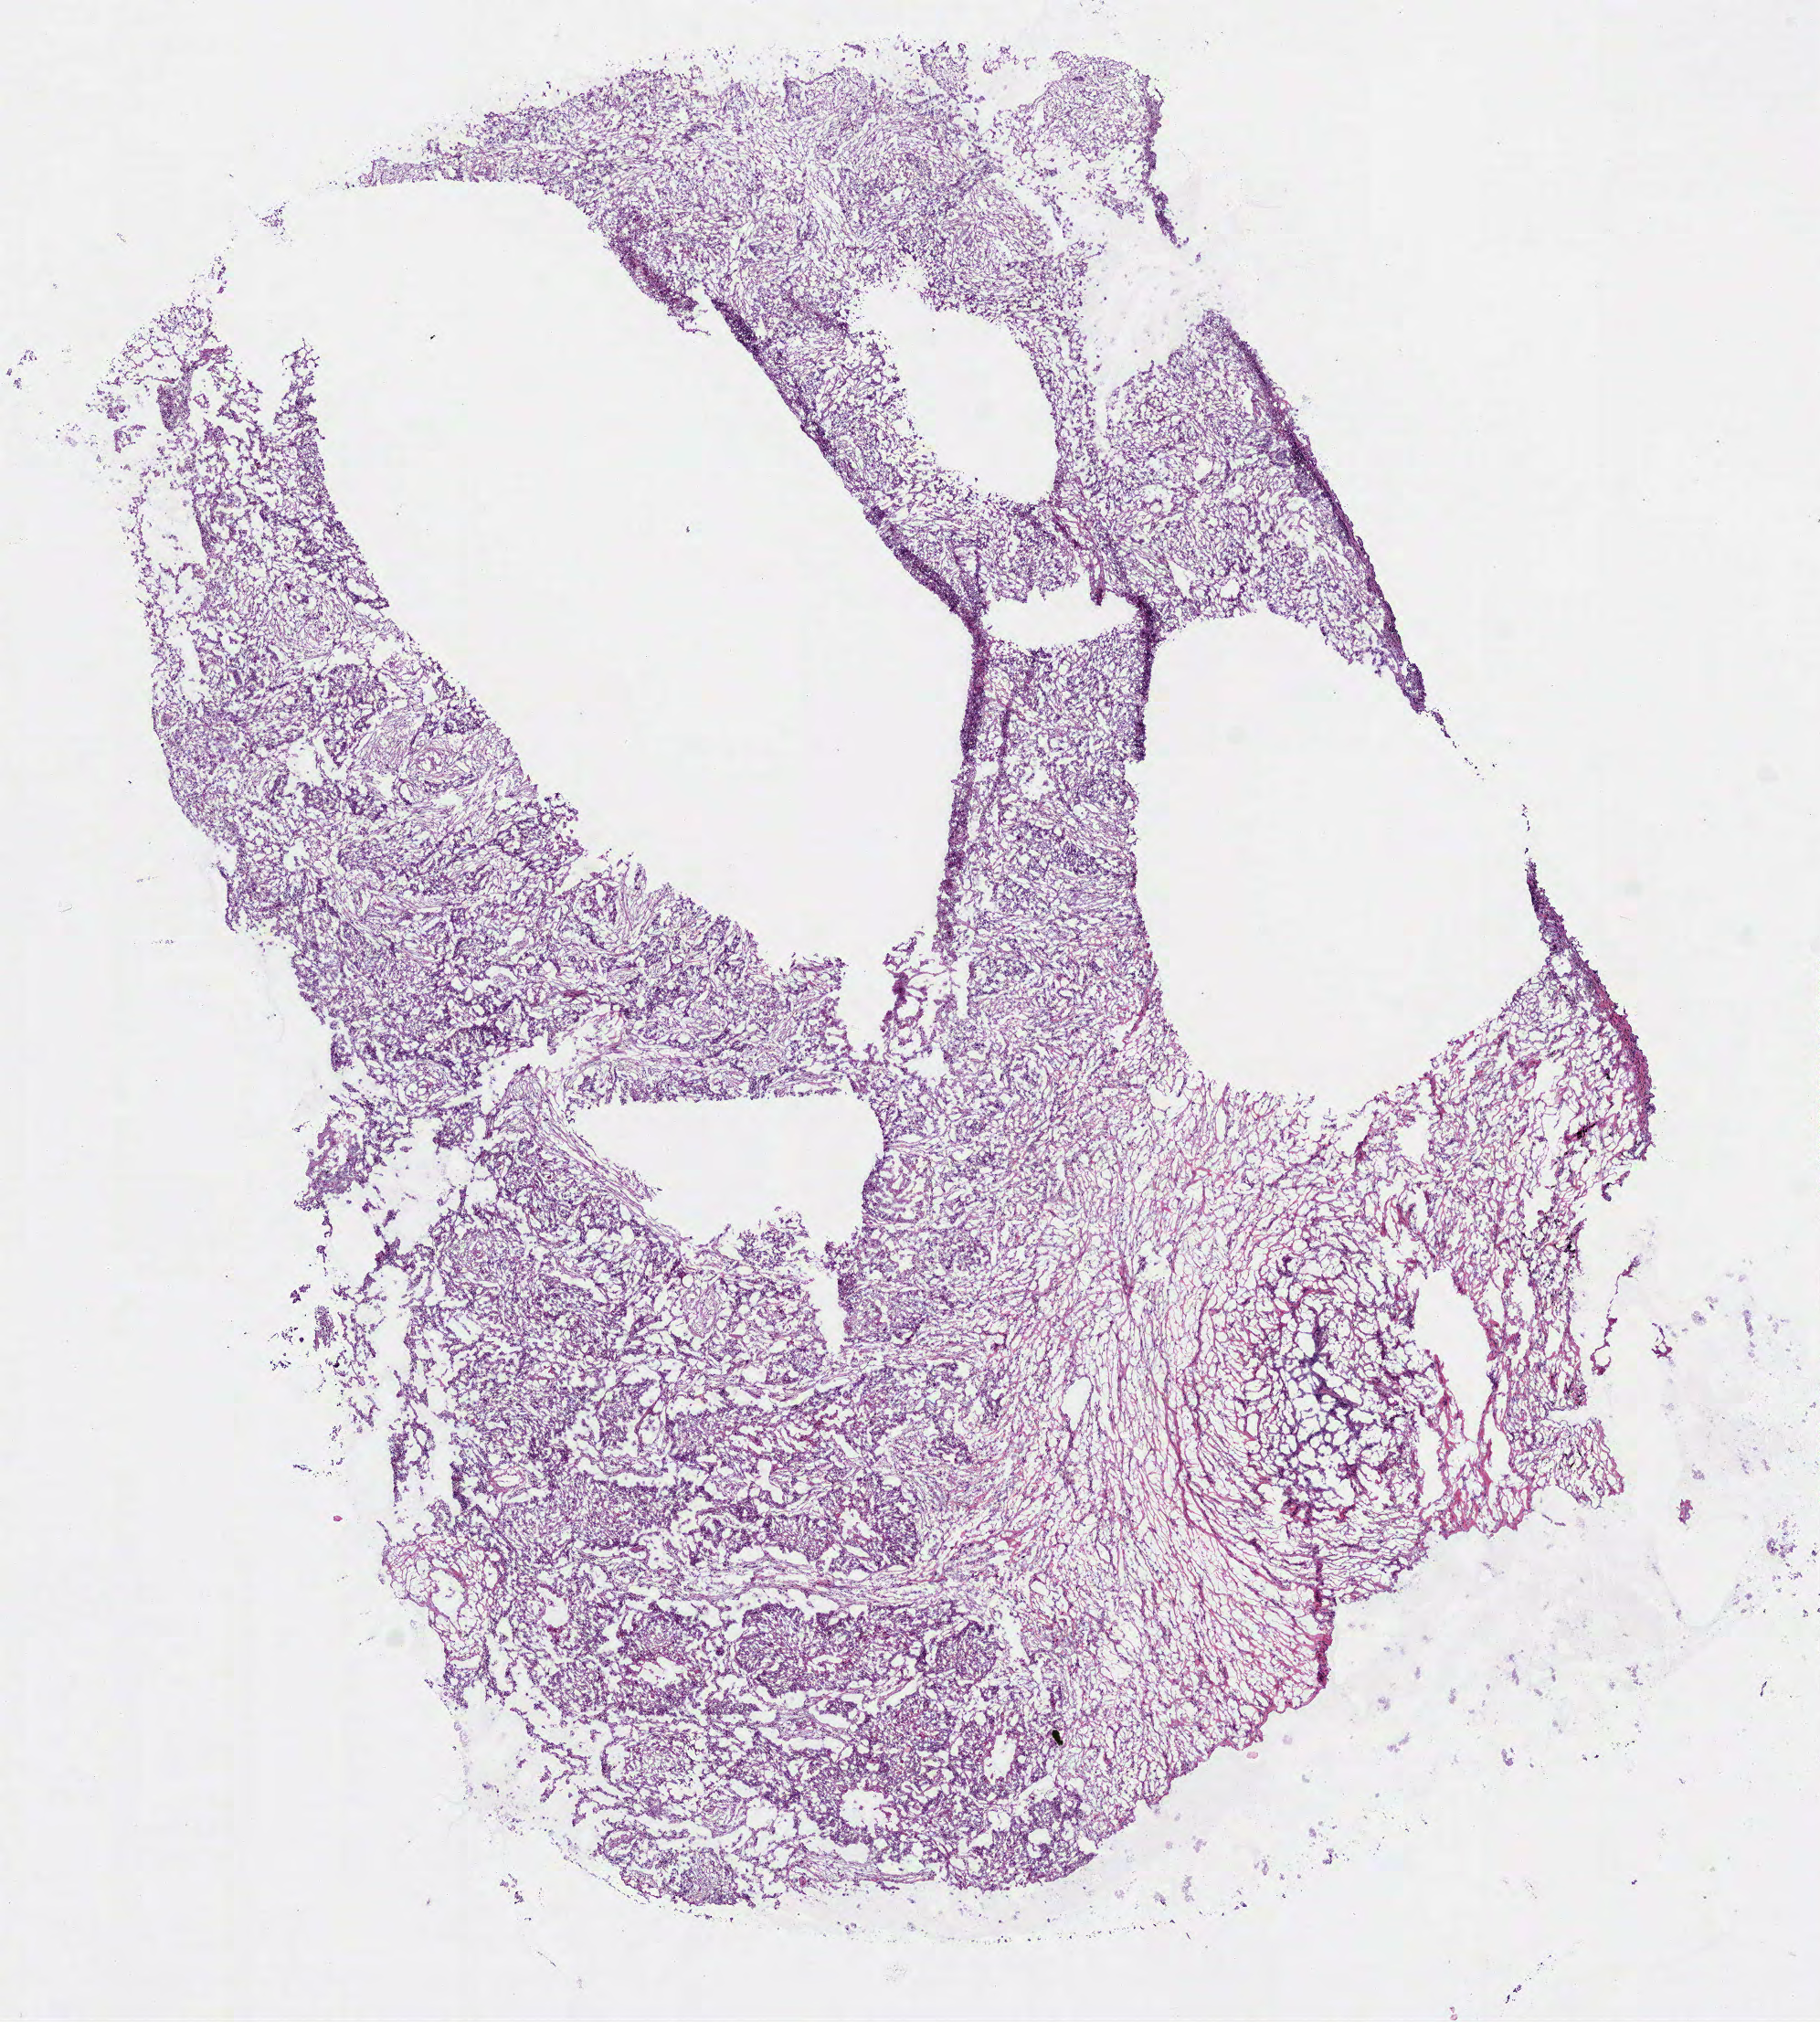
Whole-slide histology image, Hematoxylin and eosin (H&E) stained, low-resolution overview of the scanned area, about 8.0 x 8.9 mm (from a 40x scan). Frozen section. Sample: primary tumour, lung. Female, age 83 years at initial diagnosis. Pathologist review of this section (percent, as recorded): tumour cells 95%, tumour nuclei 80%, normal cells 0%, stromal cells 0%, necrosis 5%. Infiltration values recorded for this section: lymphocyte infiltration 2%, monocyte infiltration 0%, neutrophil infiltration 2%.
AJCC pathologic stage: IIB. Pathologic diagnosis: Squamous cell carcinoma, NOS (lower lobe, lung).